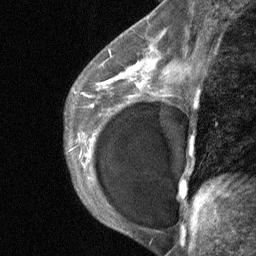
Breast MRI (dynamic contrast-enhanced), one sagittal slice; position 42 of 64 along the scan axis; dynamic contrast-enhanced study with each time point stored as its own series, time point 2 of 3 at this slice position (early post-contrast, ordered by acquisition time); 1.5 T; TE 4.8 ms, TR 27 ms; 2 mm slice thickness; 256 × 256 image matrix. Patient: female, 35 years. Case-level facts recorded for this patient, not image findings: setting: breast cancer imaged before/during neoadjuvant chemotherapy; receptor status: HR-positive, HER2-negative.
Annotated regions visible in this slice (semi-automatically segmented with operator editing):
- analysis volume of interest (the breast-tissue region the enhancement analysis was run in; not a lesion): bounding box <74,58,174,171> (left, top, right, bottom; pixels)
- tumour enhancement mask (voxels above the 90 % enhancement threshold inside the analysis volume of interest): <103,81,143,86>